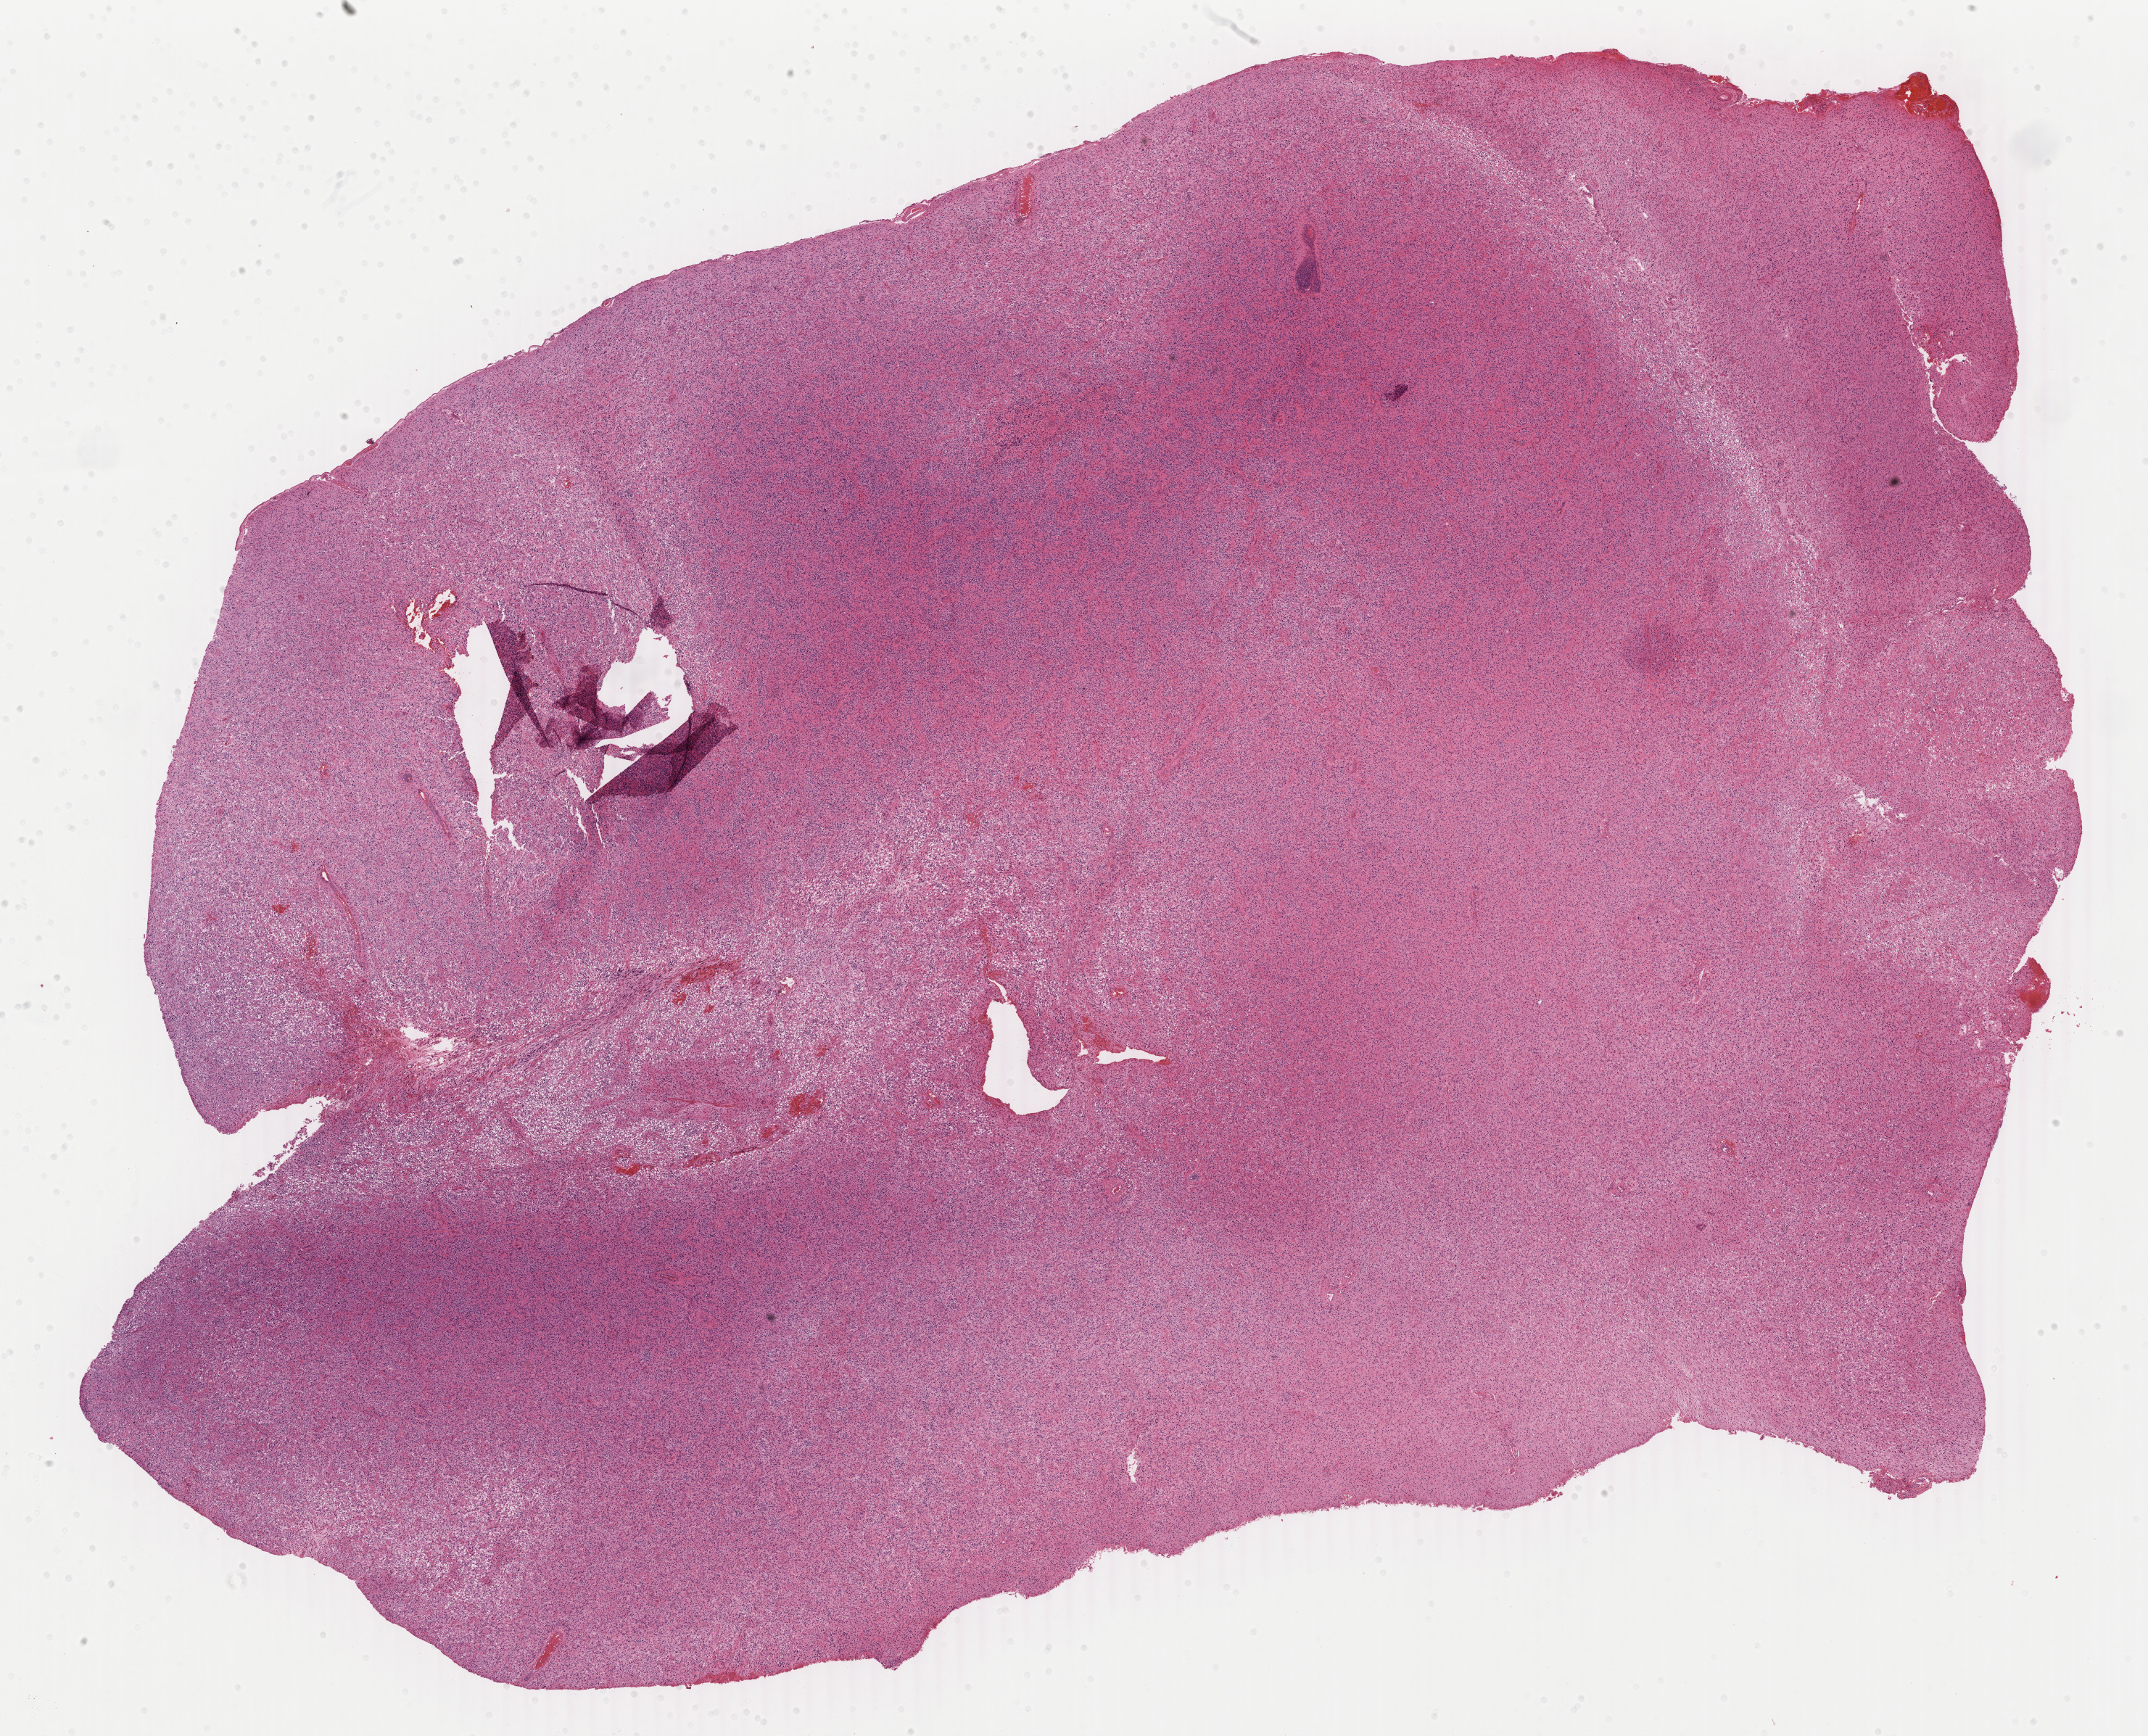
Whole-slide histology image, H&E — whole scanned area (about 23.6 x 19.0 mm, from a 40x scan) shown as a low-resolution overview, formalin-fixed paraffin-embedded (FFPE) diagnostic section, brain, primary tumour sample. Male patient; age at initial diagnosis 29 years.
Pathologic diagnosis: Astrocytoma, anaplastic (cerebrum).